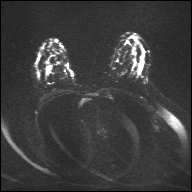
Breast MRI, one axial slice. Position 24 of 32 along the scan axis. Diffusion-weighted series; image 2 of 4 stored at this slice position (different b-values; order by instance number). 1.5 T. 4 mm slice thickness. 192 × 192 image matrix, field of view 360 × 360 mm. Female patient.
Structures marked on this image (outlined manually by an expert reader):
- tumour on diffusion-weighted imaging: bounding box [x1, y1, x2, y2] px = [46, 66, 52, 73]